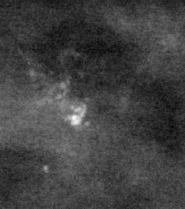
Cropped region of a digitized screen-film mammogram centred on a radiologist-marked abnormality, left breast, CC view, BI-RADS breast density category 2 (scale 1–4).
Marked abnormality: calcifications, morphology pleomorphic, distribution regional; BI-RADS assessment category 4; pathology (as recorded): benign.